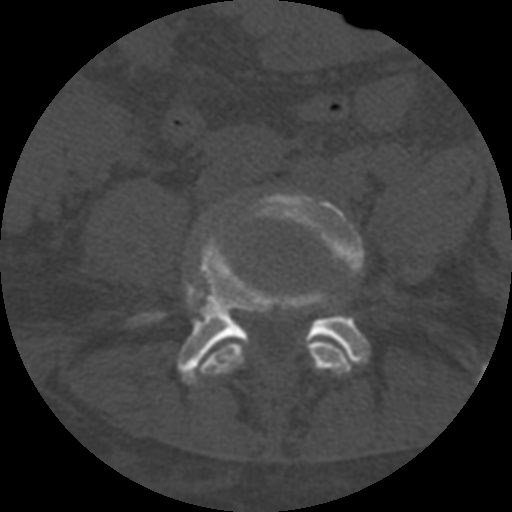
CT including the spine, one axial slice. Slice 195 of 708 in the series (ordered by position). One of 3 acquisitions stored at this slice position. Bone window (W 1800 / L 400 HU). 1.25 mm slice thickness. 512 × 512 image matrix, field of view 160 × 160 mm. Patient age 55 years. From the clinical record (not read from this slice): primary cancer: colon; vertebrae with lytic lesions (as recorded): T12, L1, L5.
Structures marked on this image (semi-automatic segmentation, software-assisted and operator-edited):
- L4 vertebra: bounding box [x1, y1, x2, y2] px = [201, 192, 364, 376]
- L5 vertebra: [126, 230, 370, 386]